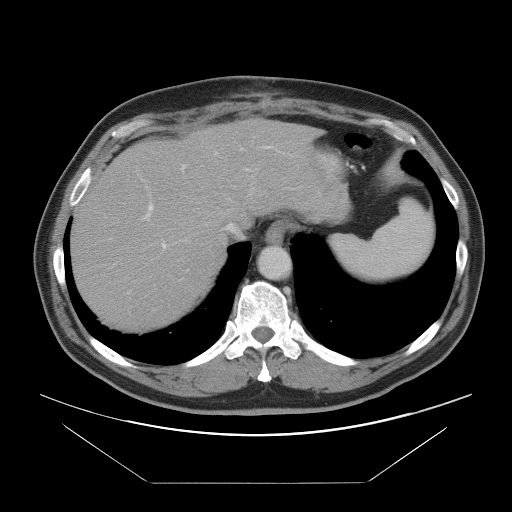
Contrast-enhanced abdominal CT, one axial slice; position 74 of 97 along the scan axis; 120 kVp; intravenous contrast given; soft-tissue window (W 400 / L 40 HU); 5 mm slice thickness; 512 × 512 image matrix, field of view 442 × 442 mm. Male patient, age 62 years. Case-level facts recorded for this patient, not image findings: diagnosis: colorectal cancer liver metastases, imaged before liver resection; multiple liver metastases: no; largest metastasis: 7 cm.
Structures marked on this image (outlined manually by an expert reader):
- hepatic veins: bounding box [x1, y1, x2, y2] px = [199, 152, 296, 234]
- liver: [73, 121, 317, 328]
- planned liver remnant (the part of the liver to remain after resection): [73, 171, 227, 327]
- portal vein (with intrahepatic branches): [128, 146, 278, 294]